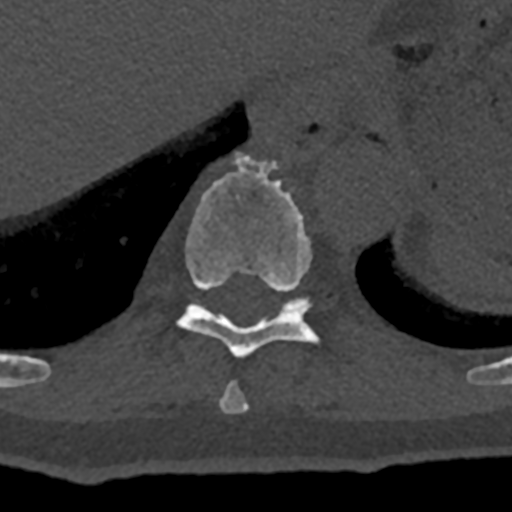
CT including the spine, one axial slice; slice 598 of 797 in the series (ordered by position); reconstruction kernel Br40s/3; 120 kVp; bone window (W 1800 / L 400 HU); 512 × 512 image matrix, field of view 160 × 160 mm. Male patient, age 74 years. From the clinical record (not read from this slice): primary cancer: renal.
Outlined on this slice (semi-automatic segmentation, software-assisted and operator-edited):
- T10 vertebra: bounding box <178,152,317,358> (left, top, right, bottom; pixels)
- T11 vertebra: <282,297,312,312>
- T9 vertebra: <219,381,249,413>